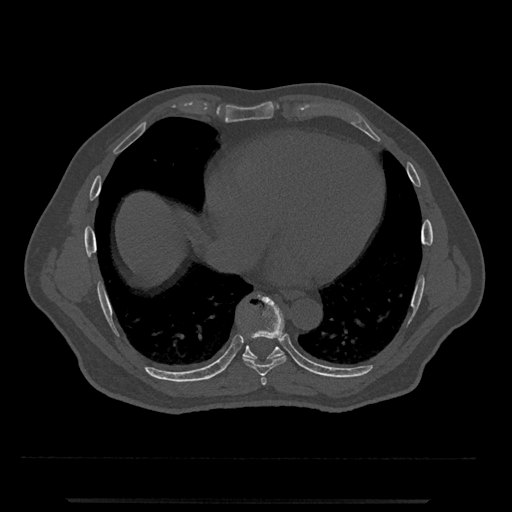
CT including the spine, one axial slice. Position 606 of 797 along the scan axis. Reconstruction kernel Br40s/3. Bone window (W 1800 / L 400 HU). 0.5 mm slice thickness. 512 × 512 image matrix, field of view 419 × 419 mm. Patient: male, 63 years. Case-level facts recorded for this patient, not image findings: primary cancer: prostate.
Outlined on this slice (semi-automatically segmented with operator editing):
- T7 vertebra: bounding box (x1, y1, x2, y2) in pixels: (261, 374, 267, 385)
- T8 vertebra: (243, 296, 286, 376)
- T9 vertebra: (222, 310, 284, 372)